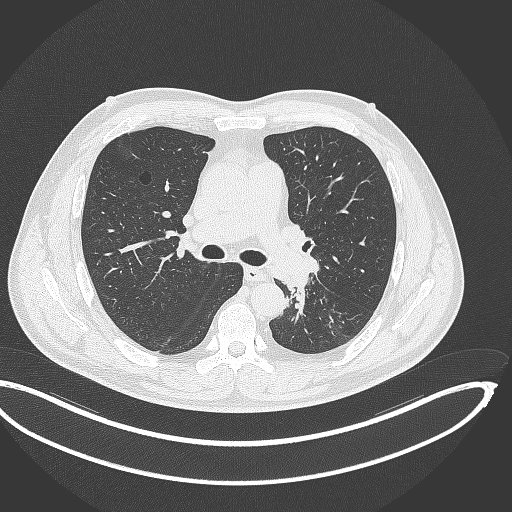
Chest CT, one axial slice. Position 217 of 362 along the scan axis. Reconstruction kernel B70f. Lung window (W 1500 / L -600 HU). 1 mm slice thickness. 512 × 512 image matrix. Male patient, age 50 years. Case-level facts recorded for this patient, not image findings: clinical TNM (as recorded): T2a N3 M0.
Outlined on this slice (rectangle marked by the reading radiologist):
- lung tumour (recorded histology: squamous cell carcinoma): bounding box <282,273,308,323> (left, top, right, bottom; pixels)